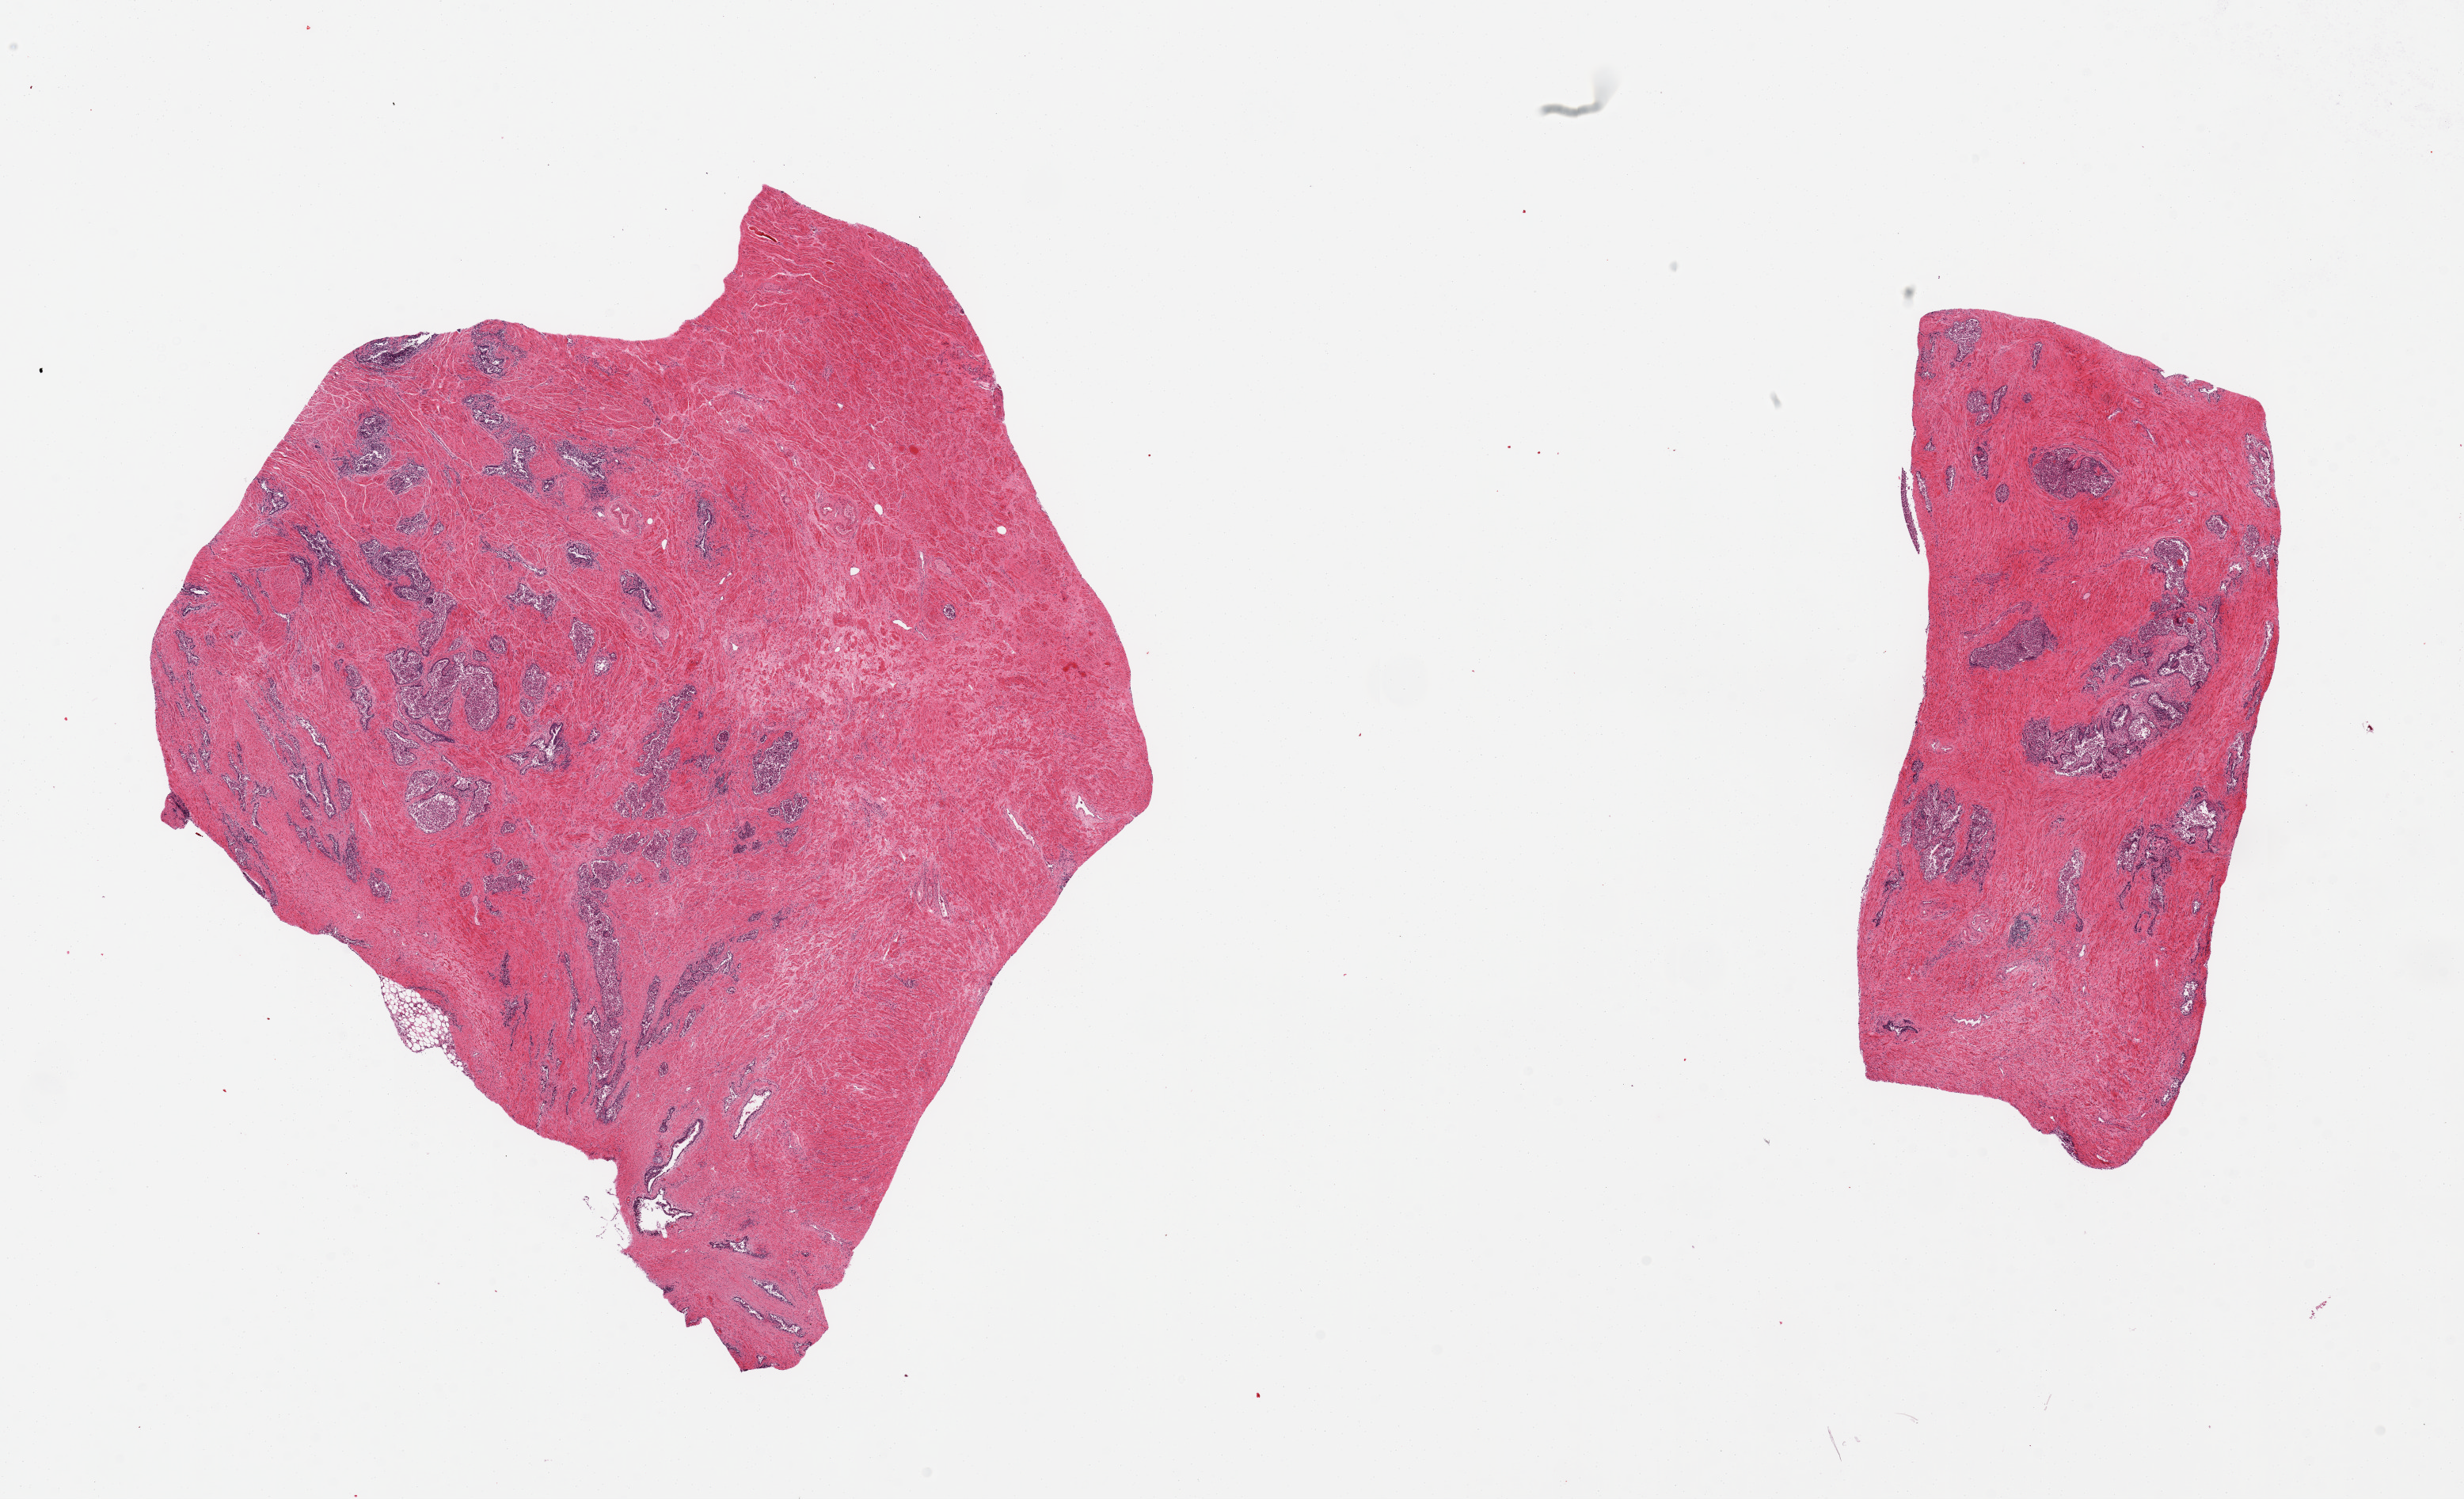
H&E whole-slide image, a low-resolution overview of the entire scanned area, about 24.6 x 15.0 mm (acquisition: 20x scan). PAXgene-fixed, paraffin-embedded tissue. Sampled site (target tissue): prostate. Tissue donor sample. Donor sex: male.
Review note (as recorded): 2 pieces, ~80% stroma, glands sloughing, acute prostatitis.